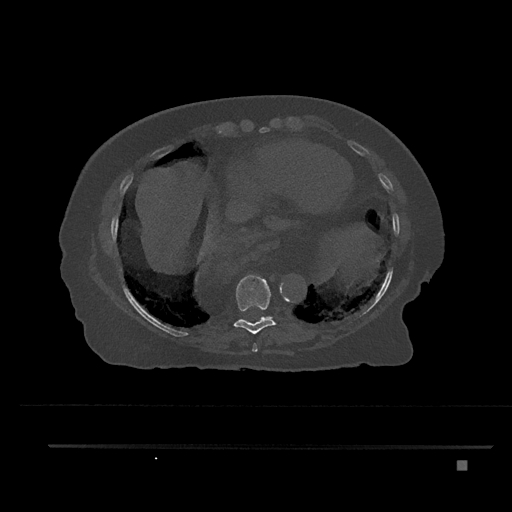
CT including the spine, one axial slice. Position 396 of 797 along the scan axis. Reconstruction kernel Br40s/3. 120 kVp. Bone window (W 1800 / L 400 HU). 512 × 512 image matrix, field of view 437 × 437 mm. Female patient, age 76 years. Case-level facts recorded for this patient, not image findings: primary cancer: lung; vertebrae with lytic lesions (as recorded): T11, L3.
Structures marked on this image (semi-automatically segmented with operator editing):
- T8 vertebra: bounding box [x1, y1, x2, y2] px = [252, 343, 258, 352]
- T9 vertebra: [234, 275, 279, 334]